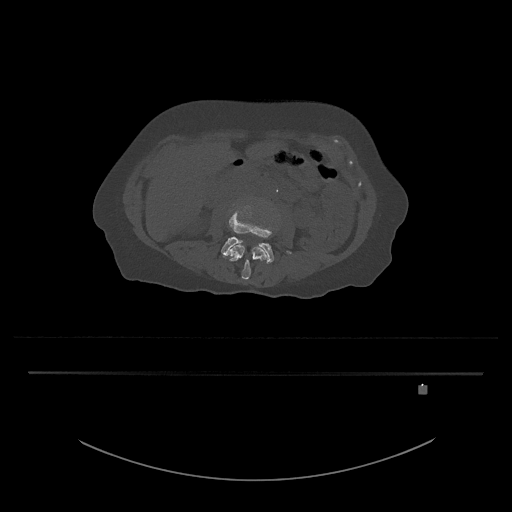
CT including the spine, one axial slice; slice 394 of 797 in the series (ordered by position); reconstruction kernel Br40s/3; 120 kVp; bone window (W 1800 / L 400 HU); 0.5 mm slice thickness; 512 × 512 image matrix, field of view 500 × 500 mm. Female patient, age 57 years. From the clinical record (not read from this slice): primary cancer: cervical.
Structures marked on this image (semi-automatic segmentation, software-assisted and operator-edited):
- L3 vertebra: box from (x=226, y=243) to (x=267, y=280) px
- L4 vertebra: (x=221, y=206)–(x=291, y=264)